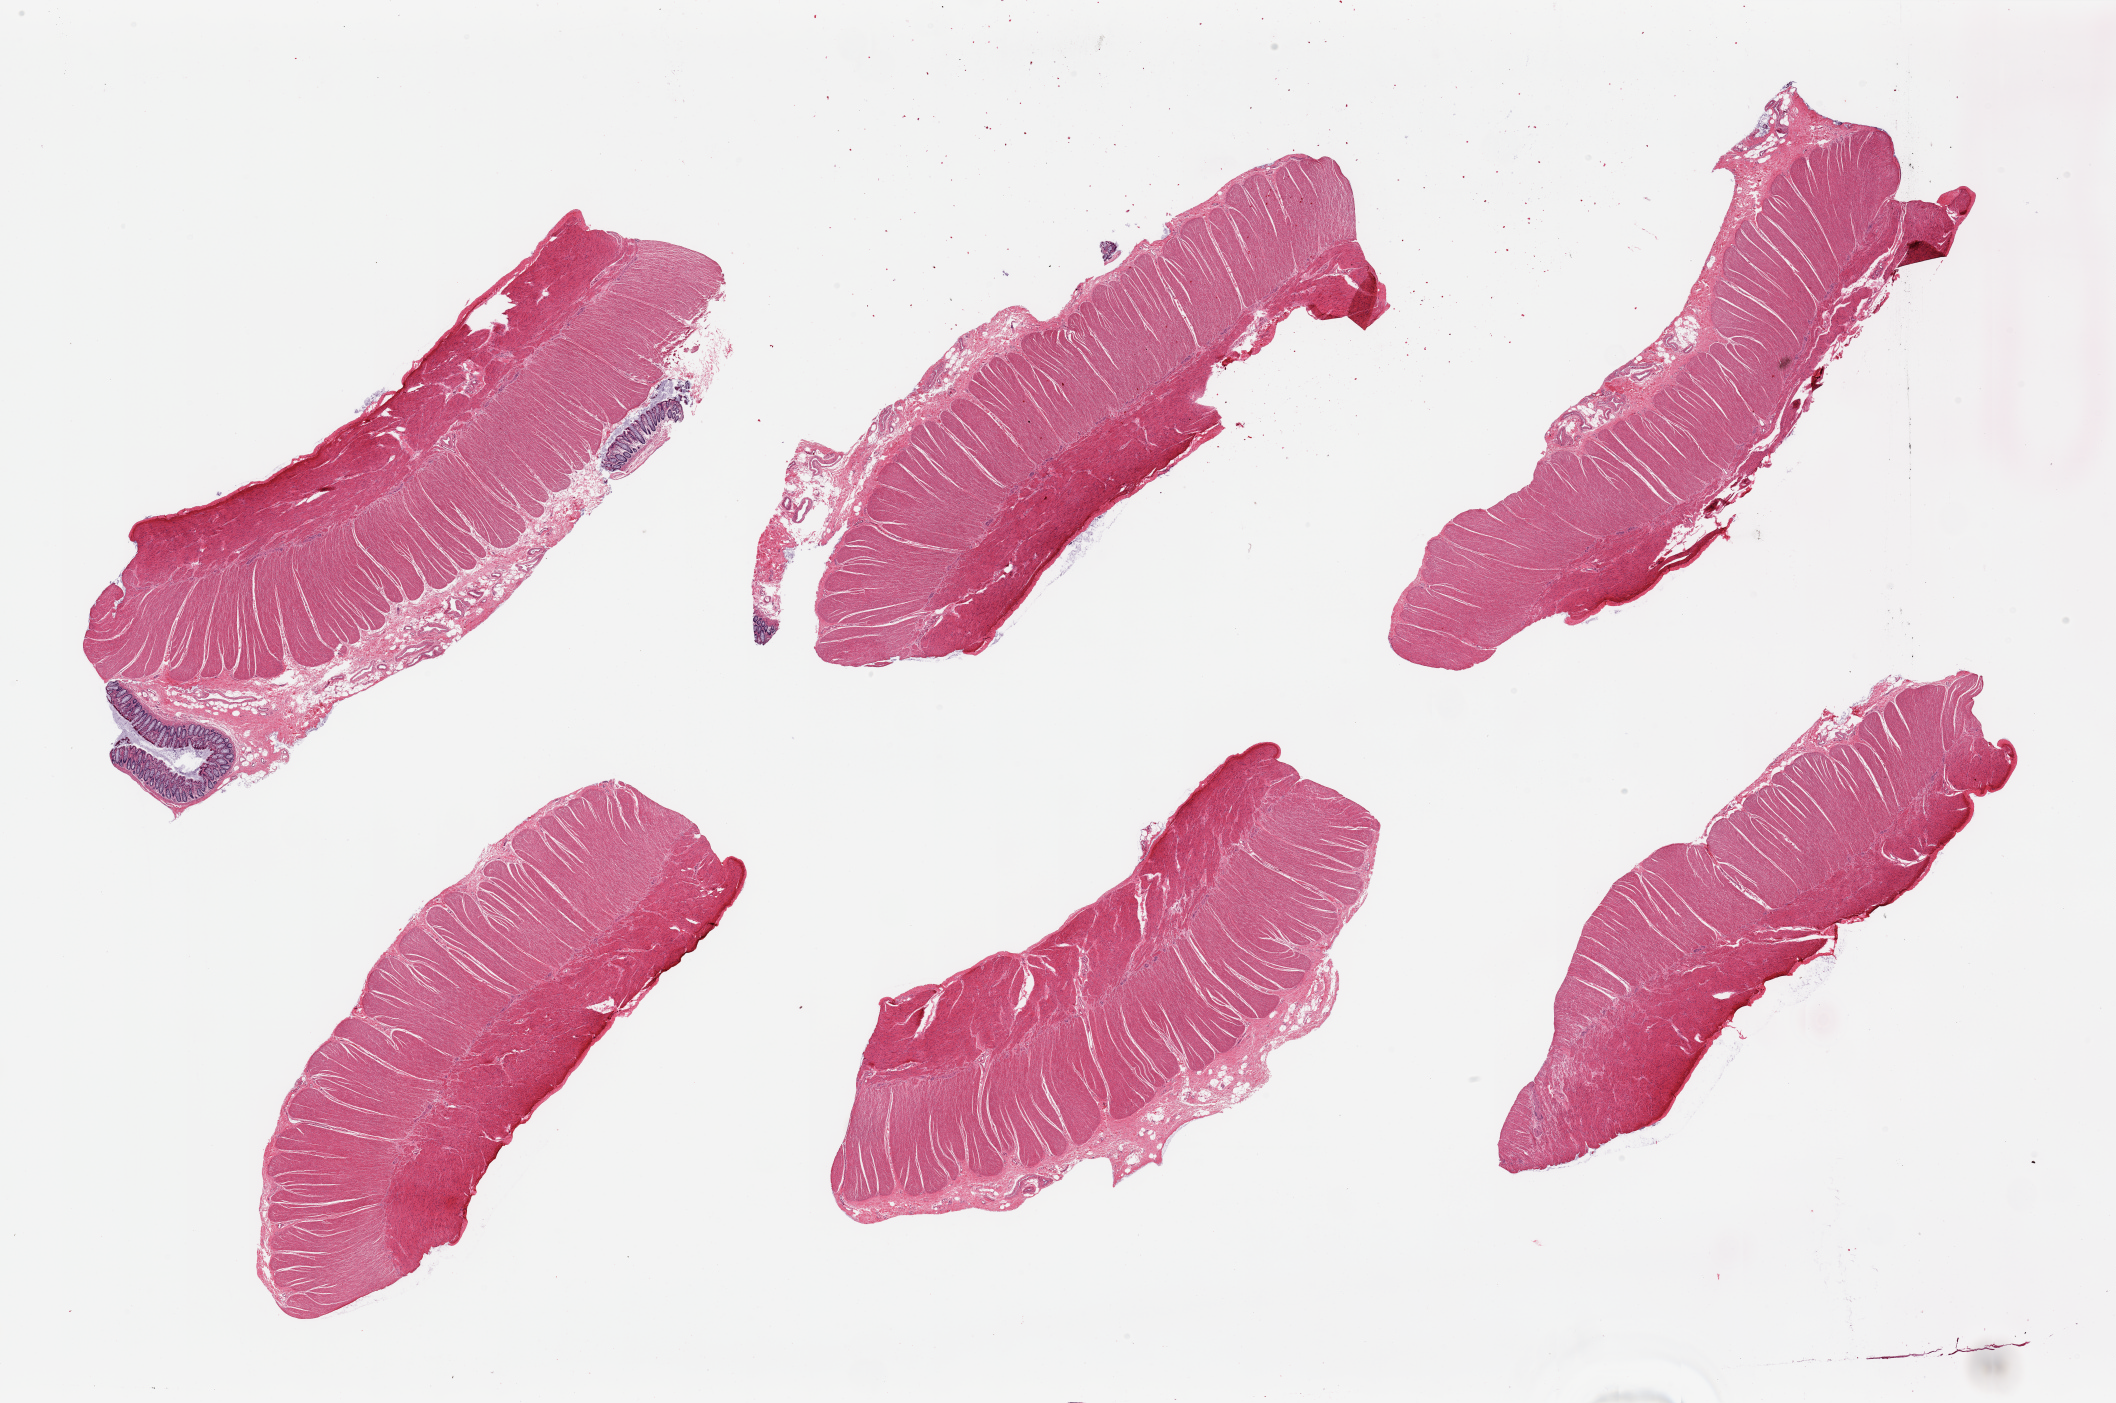
Haematoxylin and eosin whole-slide image, brightfield — a low-resolution overview of the entire scanned area, about 33.5 x 22.2 mm, PAXgene-fixed, paraffin-embedded tissue, section of sigmoid colon (target tissue), tissue donor sample. Donor sex: male.
Pathologist's review note for this sample: 6 pieces, target muscularis, few minute foci of 'contaminant' mucosa.